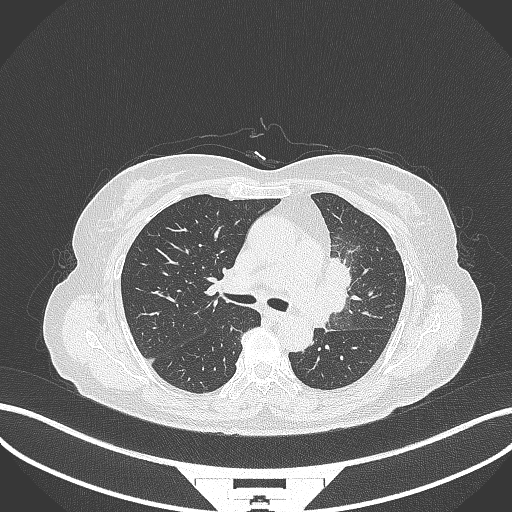
Chest CT, one axial slice. Position 208 of 382 along the scan axis. Reconstruction kernel B70f. 120 kVp. Lung window (W 1500 / L -600 HU). 1 mm slice thickness. 512 × 512 image matrix, field of view 400 × 400 mm. Female patient, age 64 years. From the clinical record (not read from this slice): clinical TNM (as recorded): T2a N2 M0.
Outlined on this slice (rectangle marked by the reading radiologist):
- lung tumour (recorded histology: adenocarcinoma): bounding box [x1, y1, x2, y2] px = [314, 257, 352, 316]